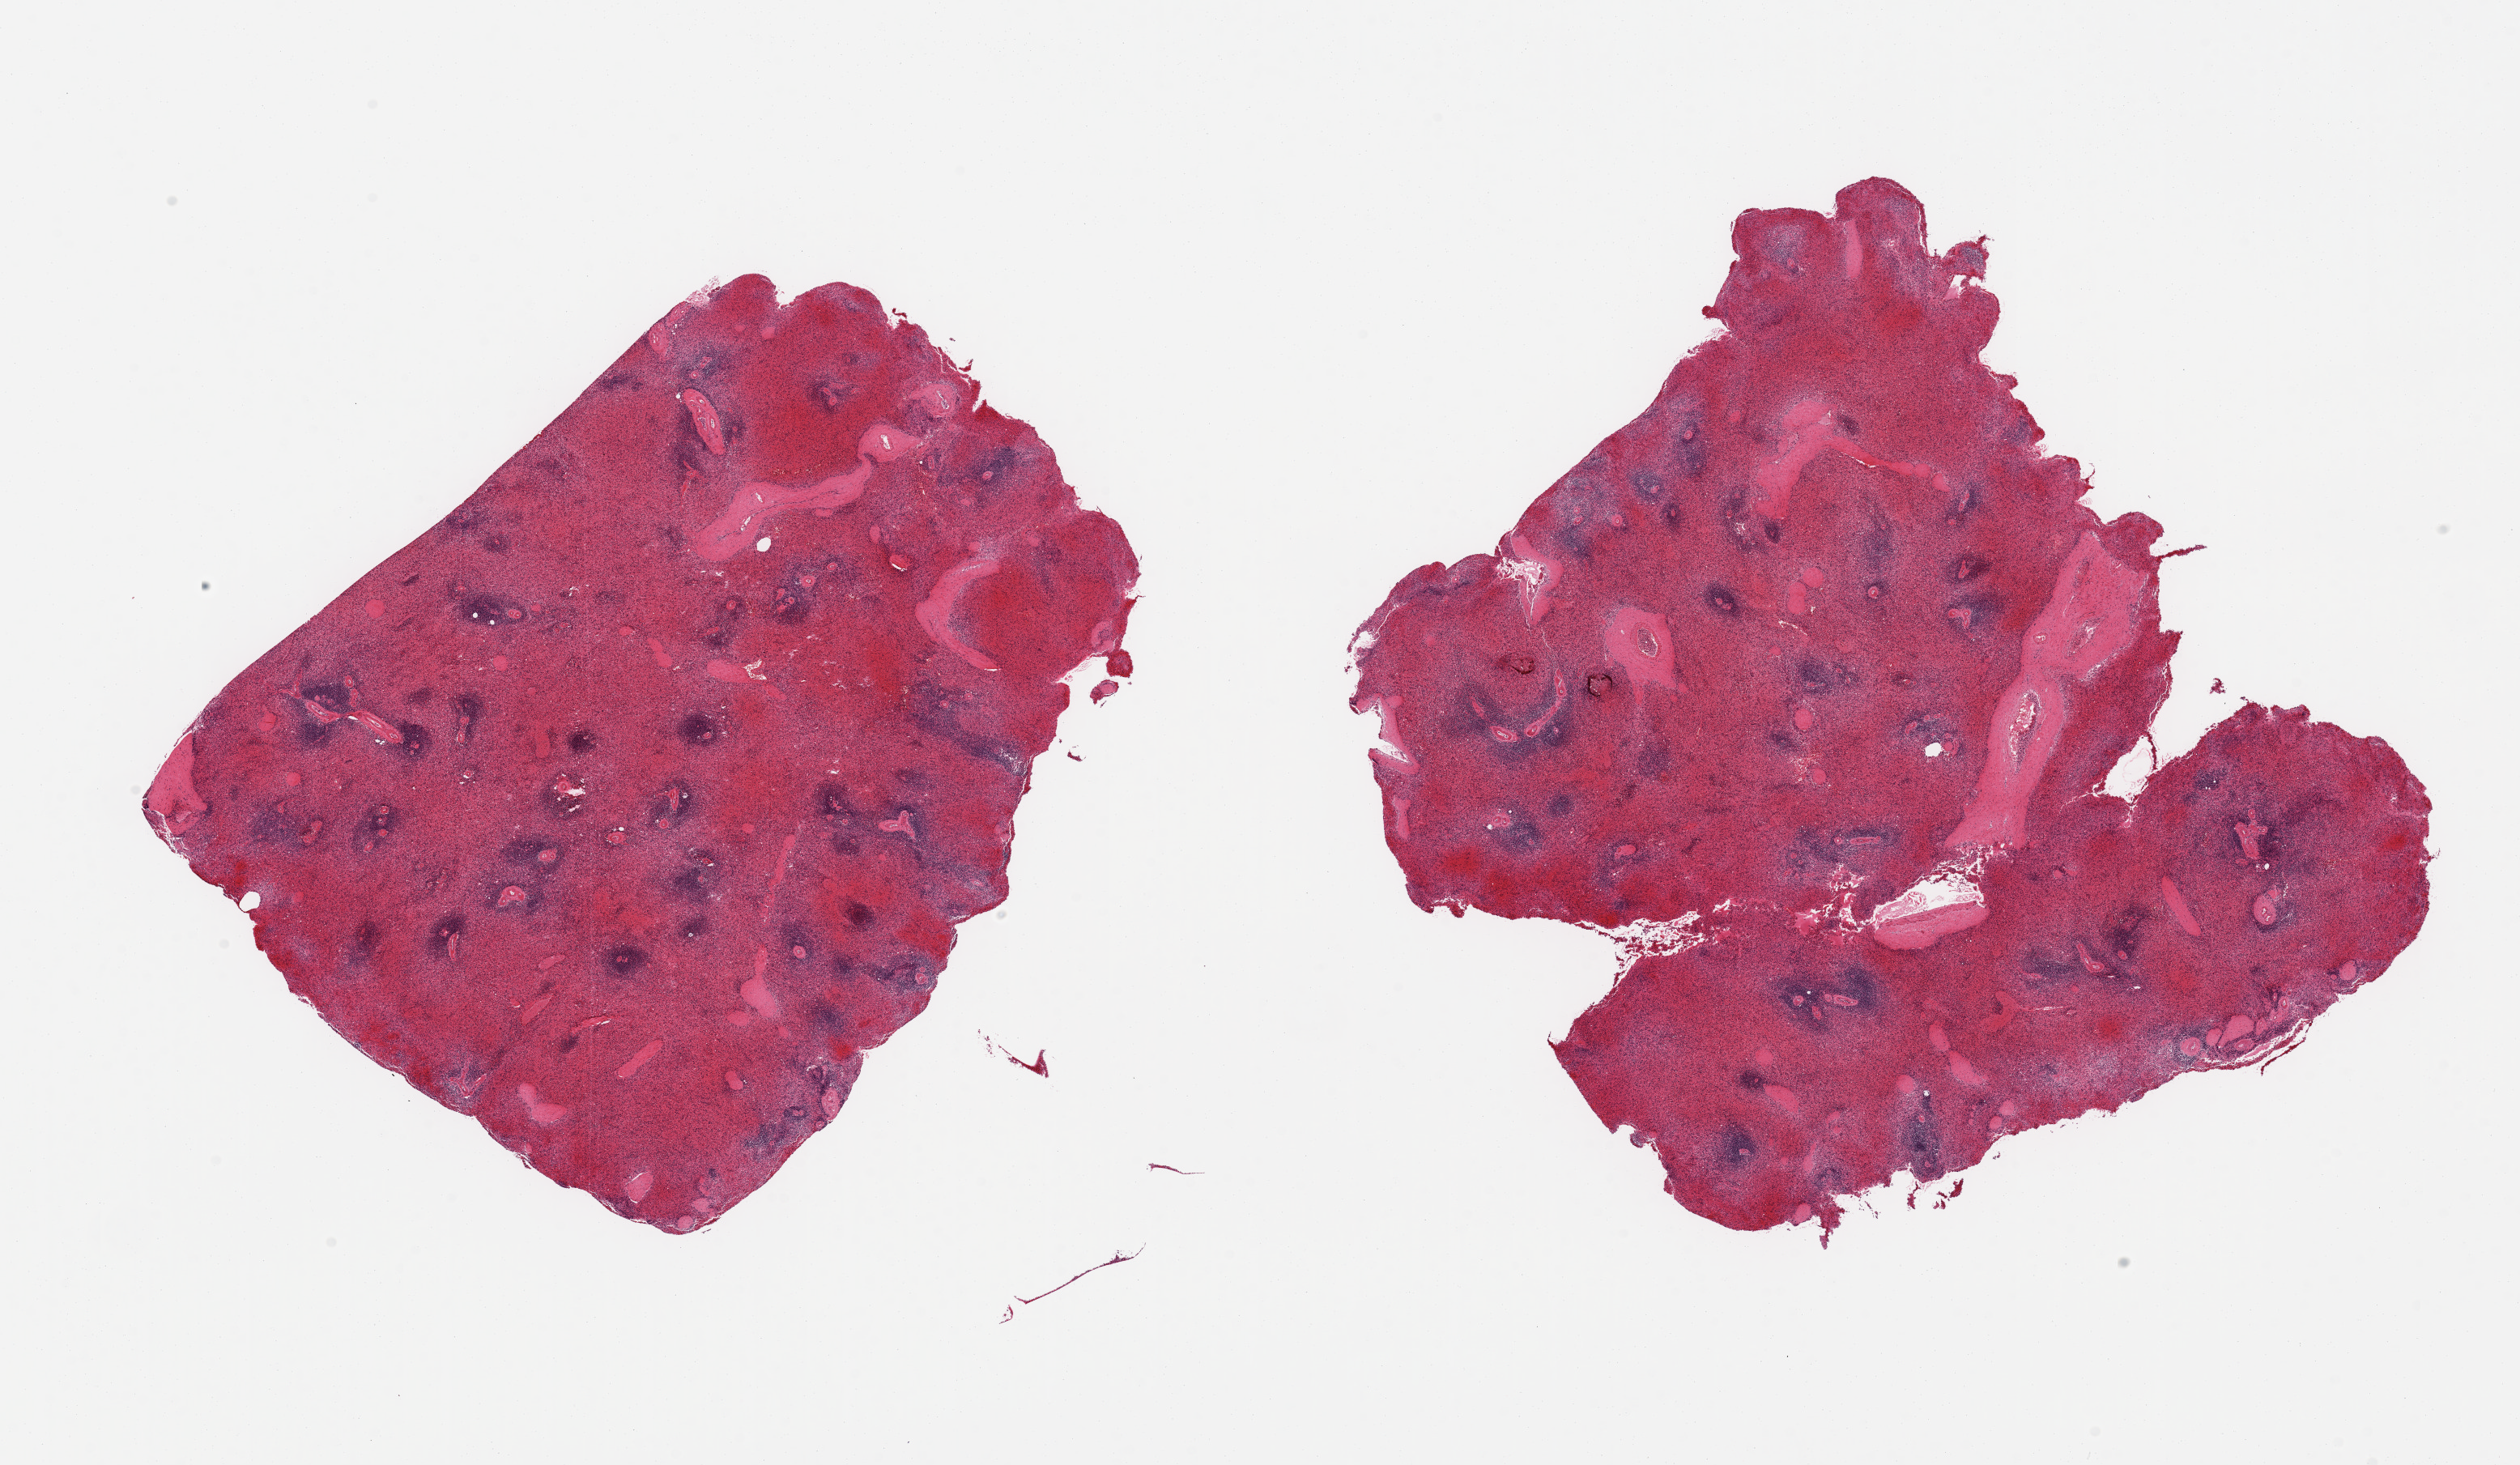
Whole-slide image, haematoxylin and eosin stain, whole scanned area (about 24.6 x 14.3 mm, slide scanned at 20x) shown as a low-resolution overview. PAXgene-fixed paraffin-embedded (PFPE) section. Section of spleen (target tissue). Donor tissue sample. Donor sex: male.
Review note (as recorded): 2 pieces; severely congested.